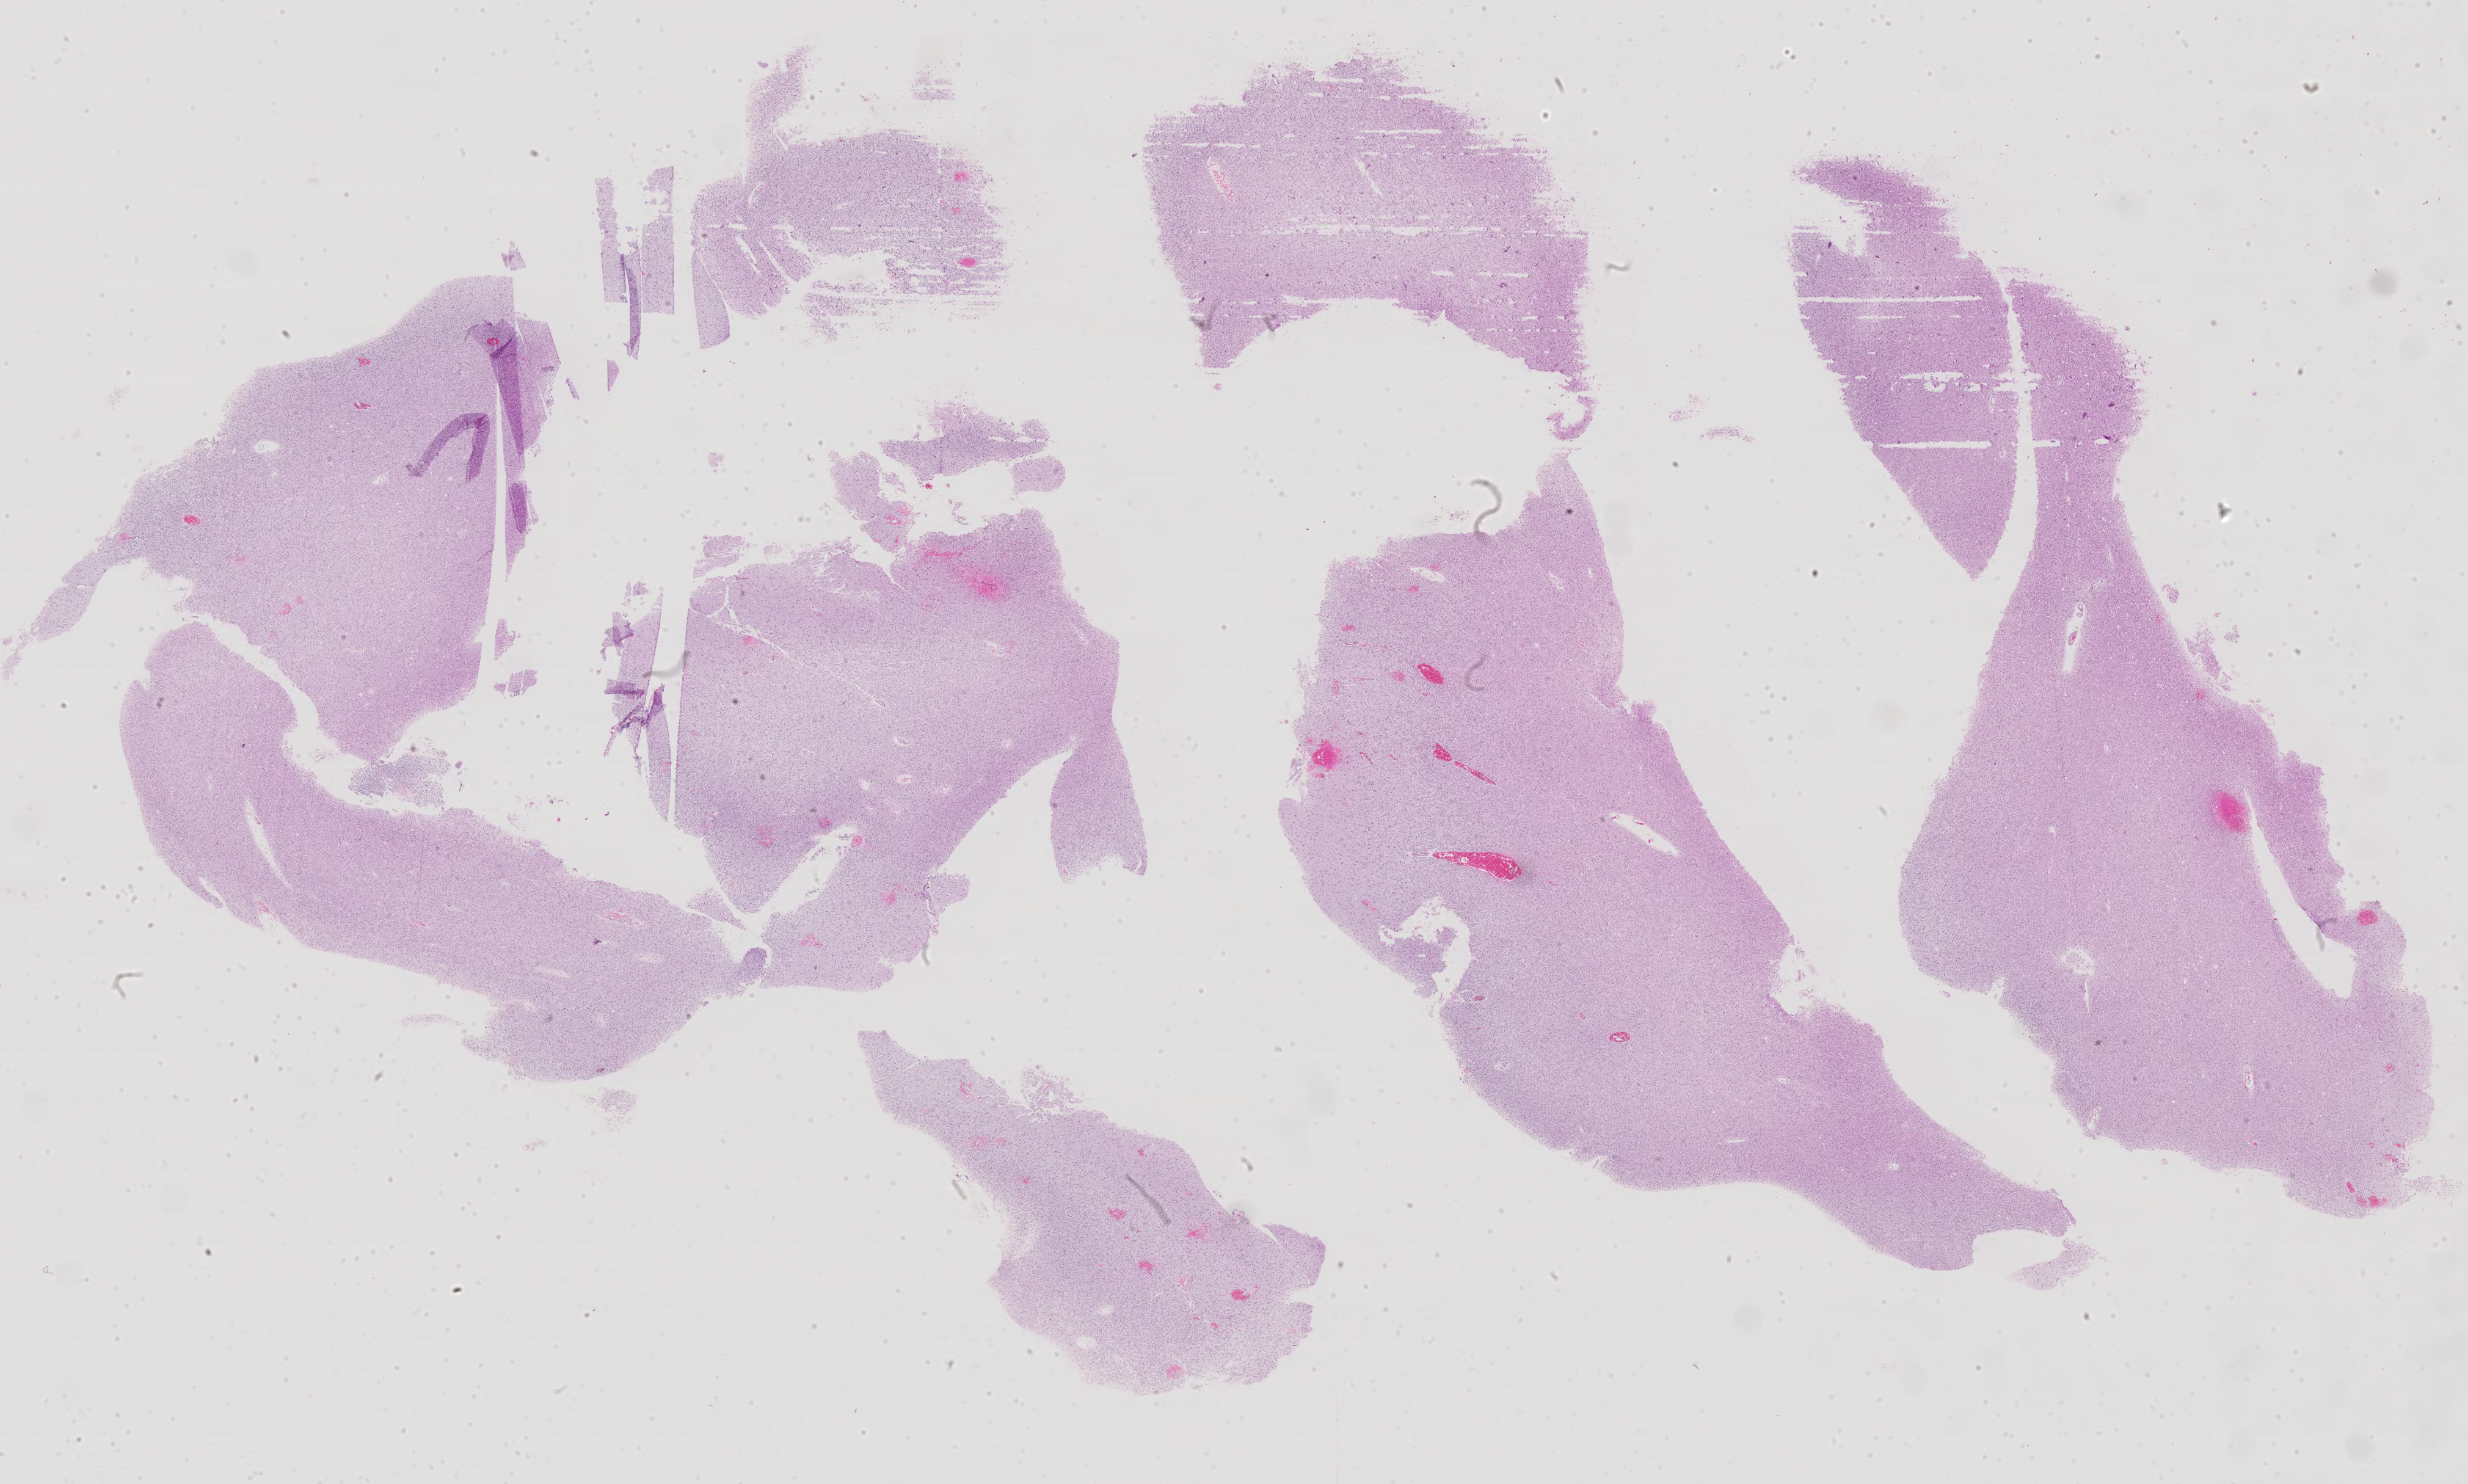
Digitized H&E tissue section (whole slide), shown as a low-resolution overview of the whole scanned area (about 32.3 x 19.4 mm); formalin-fixed paraffin-embedded (FFPE) diagnostic section; sample: primary tumour, brain. Female patient; age at initial diagnosis 27 years. Histologic grade: G2 (moderately differentiated).
• pathologic diagnosis: Oligodendroglioma, NOS (cerebrum)
• laterality: right